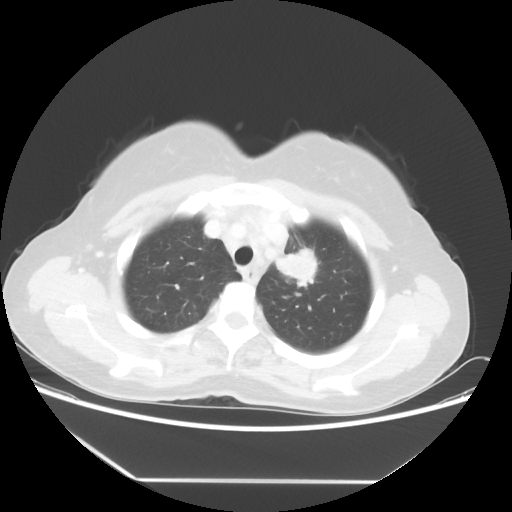
Chest CT, one axial slice. Position 43 of 52 along the scan axis. Reconstruction kernel STANDARD. Lung window (W 1500 / L -600 HU). 5 mm slice thickness. 512 × 512 image matrix. Female patient, age 50 years. Case-level facts recorded for this patient, not image findings: clinical TNM (as recorded): T2 N3 M0.
Outlined on this slice (bounding box drawn by a radiologist):
- lung tumour (recorded histology: adenocarcinoma): bounding box [x1, y1, x2, y2] px = [267, 234, 319, 294]